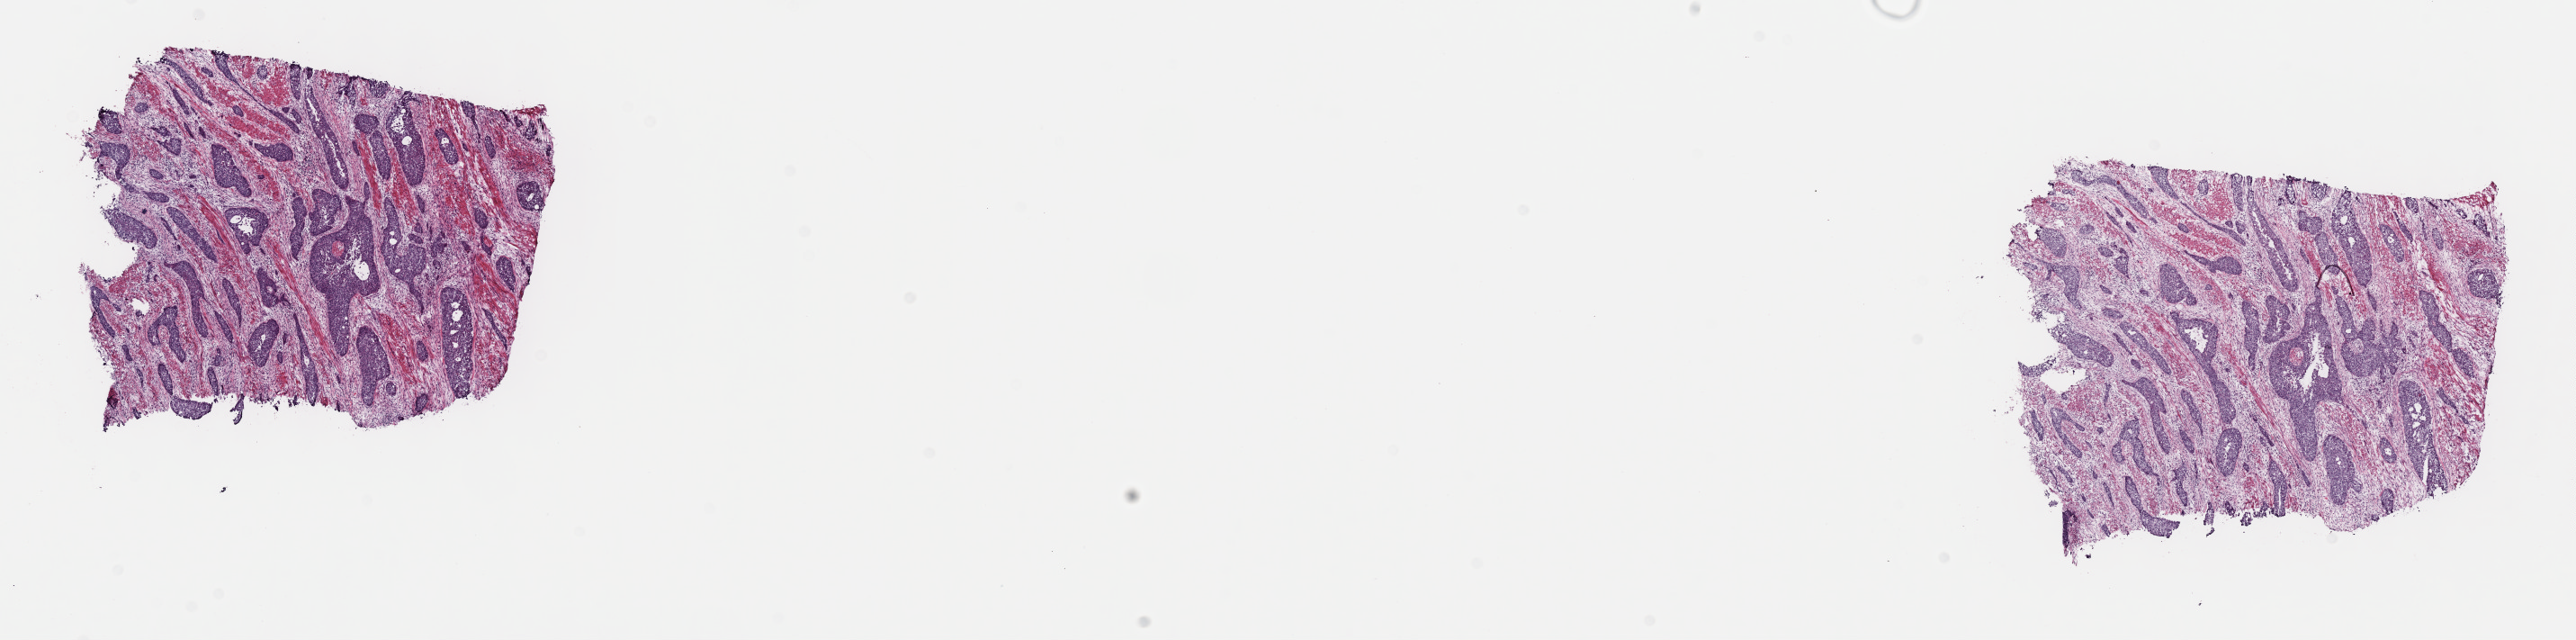
Whole-slide histology image, H&E, low-resolution overview of the scanned area, about 23.2 x 5.8 mm (acquisition: 40x scan); frozen section from the top of the tissue portion; sample: primary tumour, bladder. Male, age 76 years at initial diagnosis. Histologic grade: high grade. Pathologist review of this section (percent, as recorded): tumour cells 75%, tumour nuclei 75%, normal cells 0%, stromal cells 25%, necrosis 0%. Infiltration values recorded for this section: lymphocyte infiltration 2%, monocyte infiltration 1%, neutrophil infiltration 4%.
Pathologic diagnosis: Transitional cell carcinoma. AJCC pathologic stage: IV. Lymph nodes positive (case pathology): 2 of 36 examined.